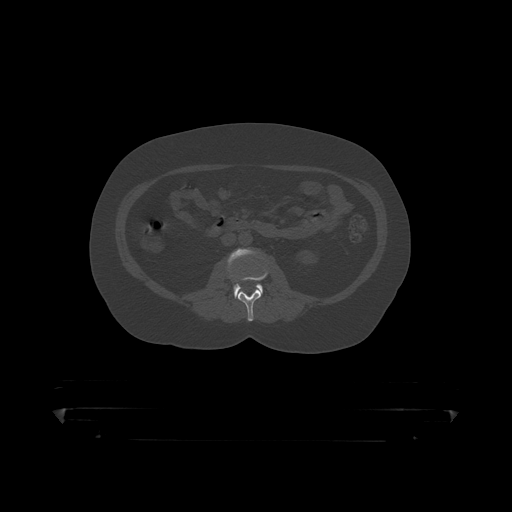
CT including the spine, one axial slice. Slice 106 of 390 in the series (ordered by position). Bone window (W 1800 / L 400 HU). 512 × 512 image matrix, field of view 650 × 650 mm. Patient: male, 60 years. From the clinical record (not read from this slice): primary cancer: prostate.
Annotated regions visible in this slice (semi-automatic segmentation, software-assisted and operator-edited):
- L2 vertebra: bounding box <230,267,269,319> (left, top, right, bottom; pixels)
- L3 vertebra: <228,249,263,298>